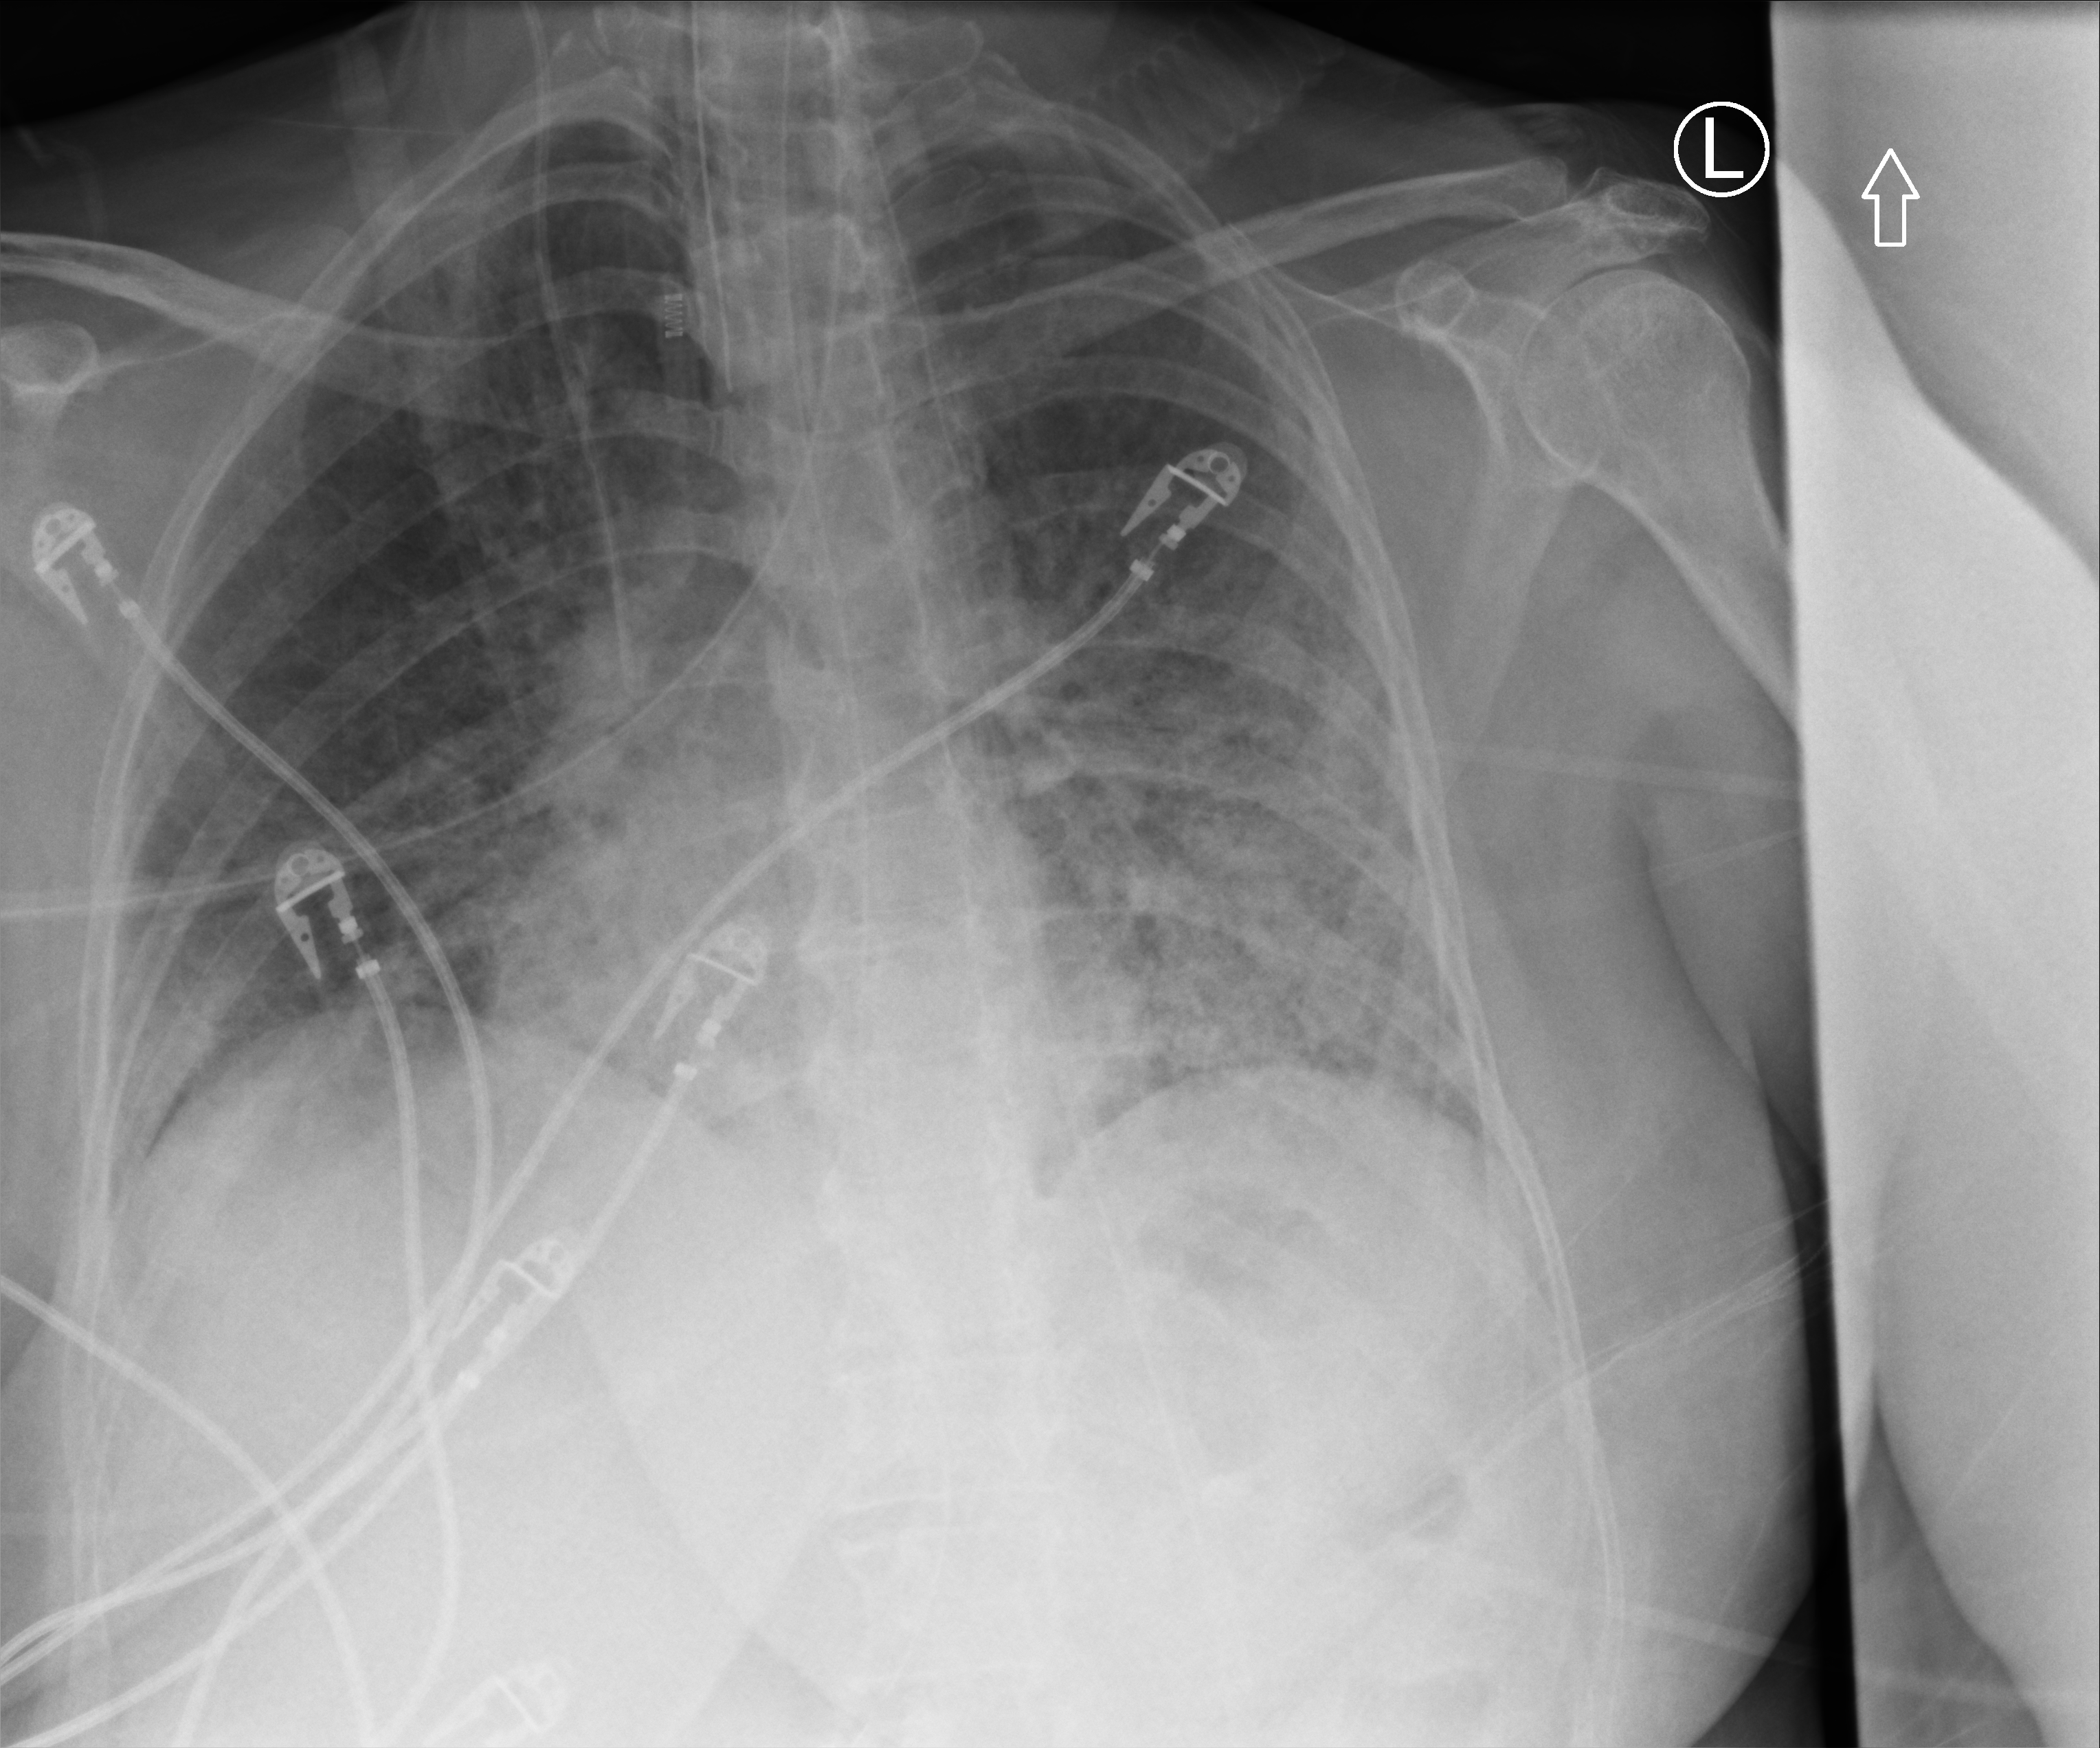
Portable chest radiograph; anteroposterior (AP) projection. Patient hospitalised with COVID-19; female, aged 60–74 years.
From the hospital-stay record, not from the radiograph (when in the stay this image was taken is not recorded): hypertension (admission record): yes; length of hospital stay: 43 days.